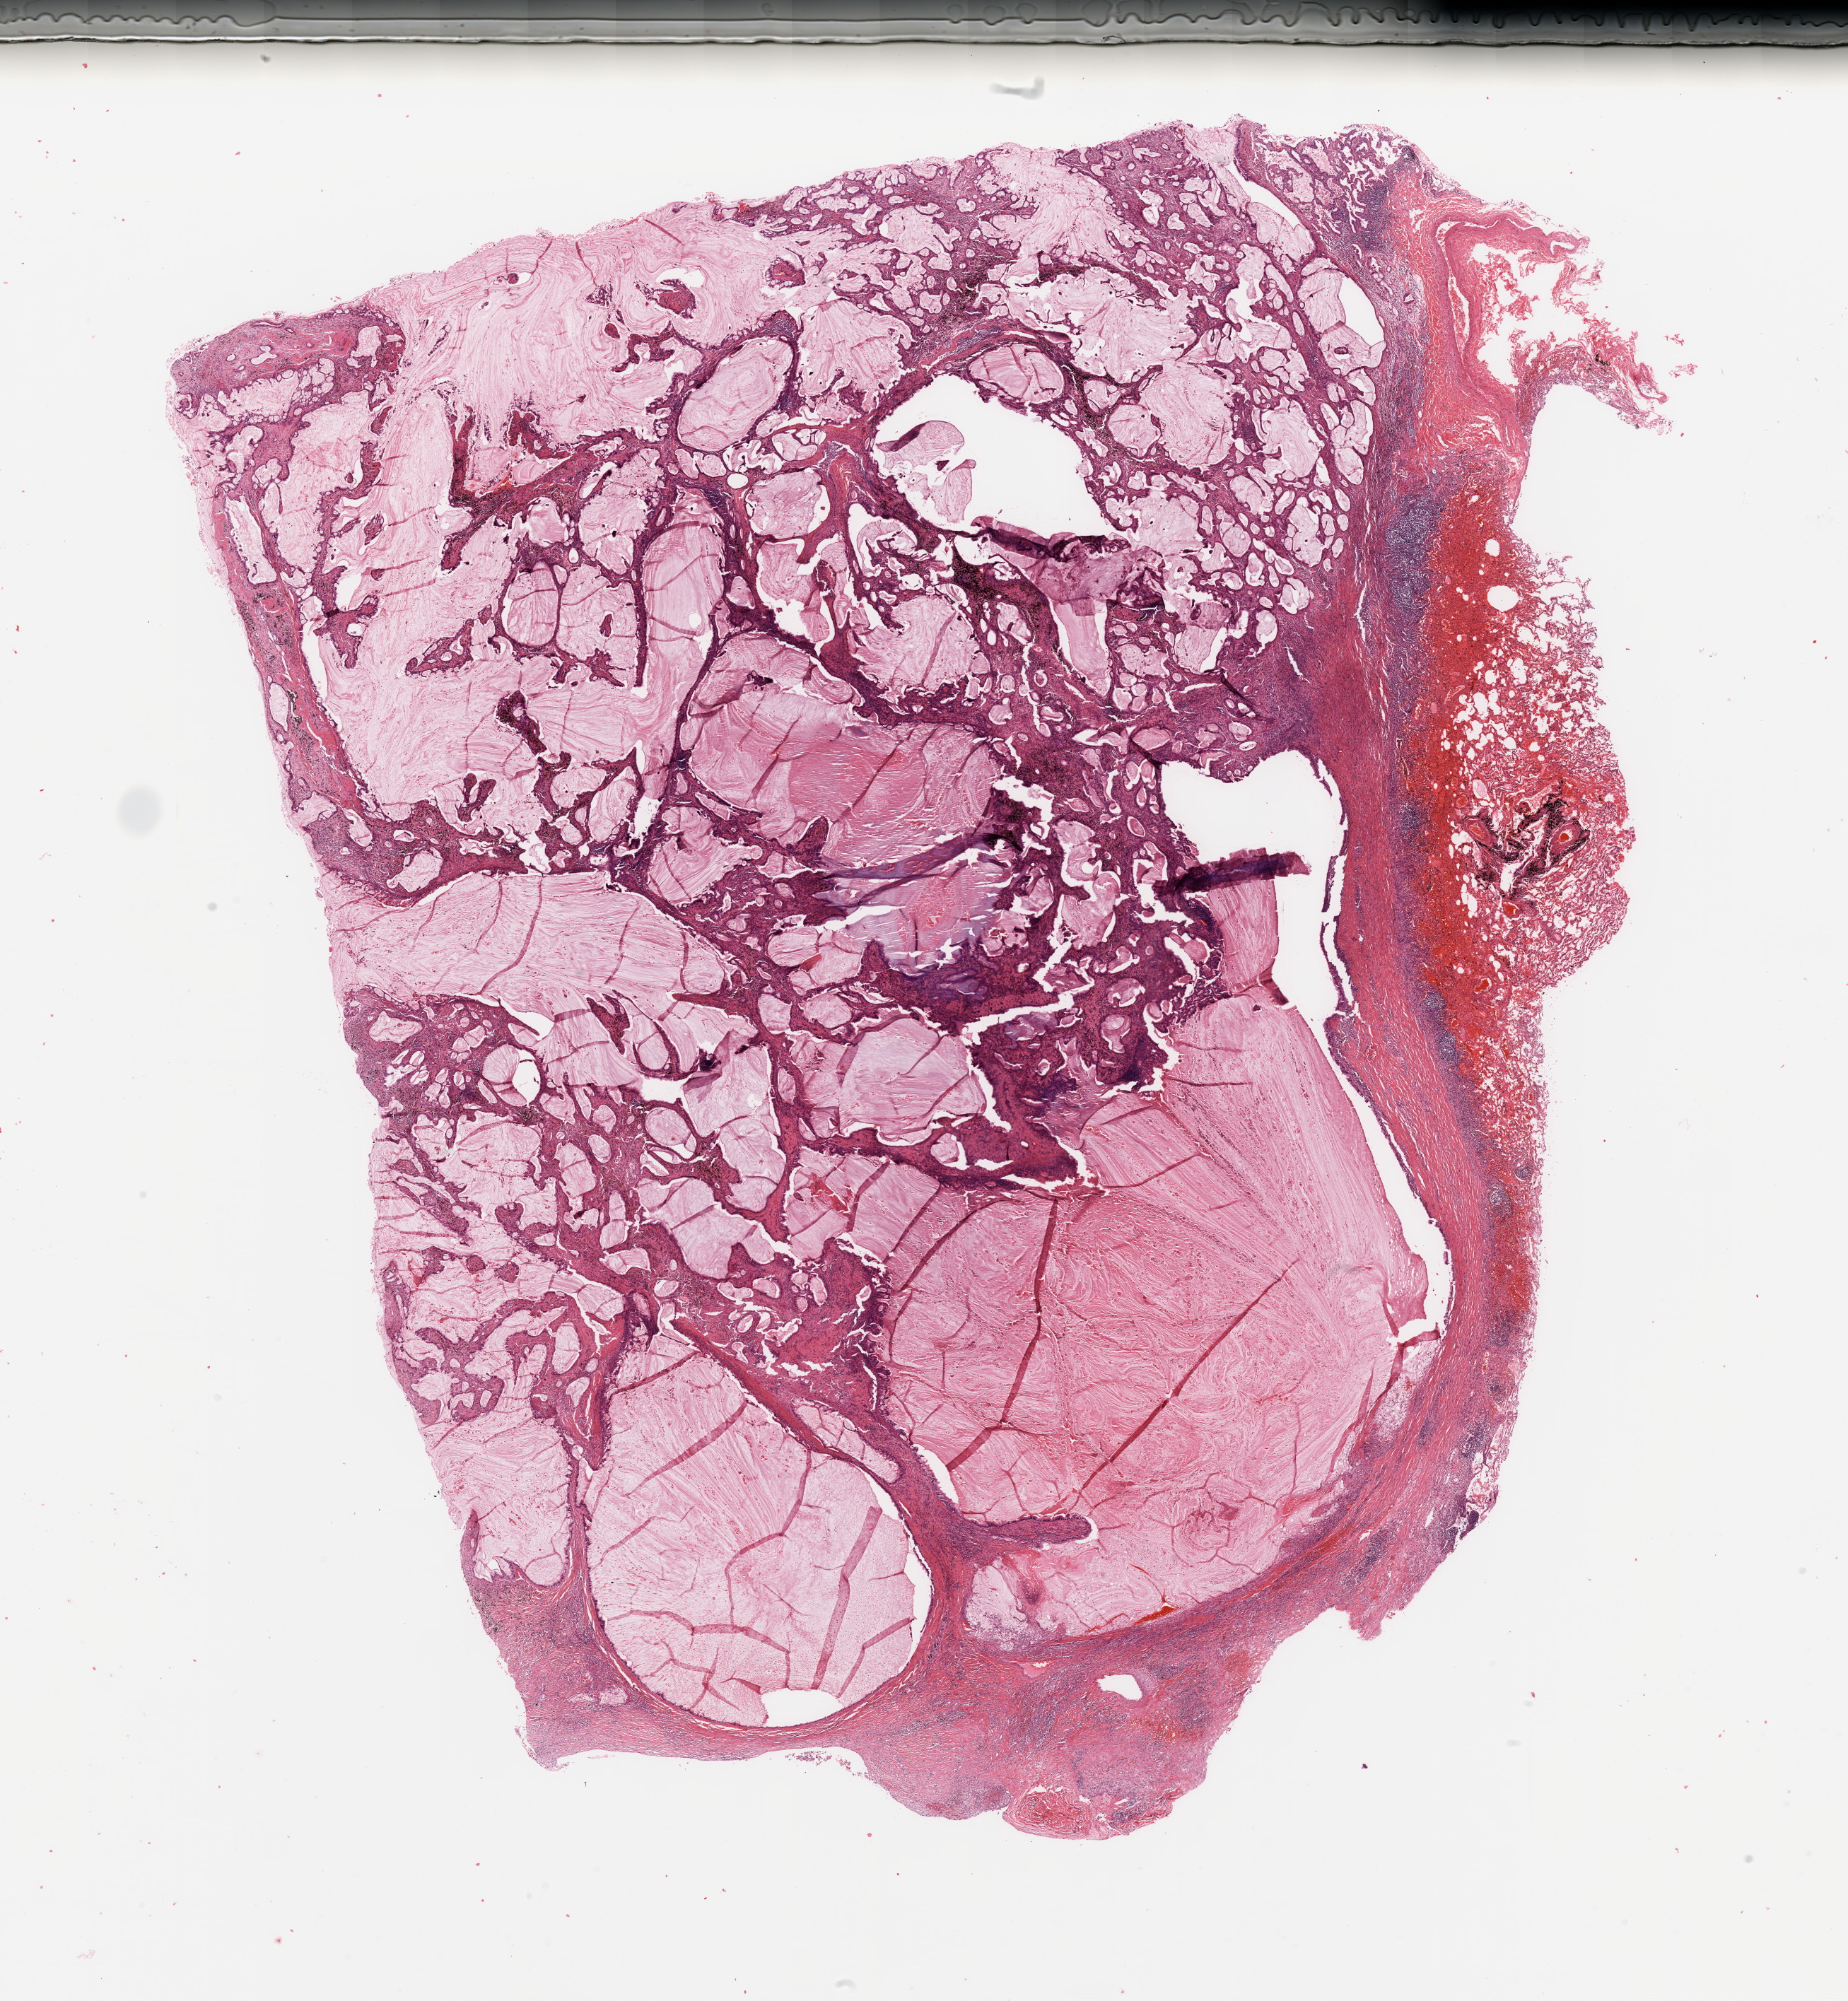
Hematoxylin and eosin (H&E) stained whole-slide image — a low-resolution overview of the entire scanned area, about 20.7 x 22.4 mm, tumour tissue sample, lung. 60-year-old male patient. Histologic grade: G2 (moderately differentiated).
* AJCC pathologic stage: IIB
* histologic diagnosis: Adenocarcinoma, NOS